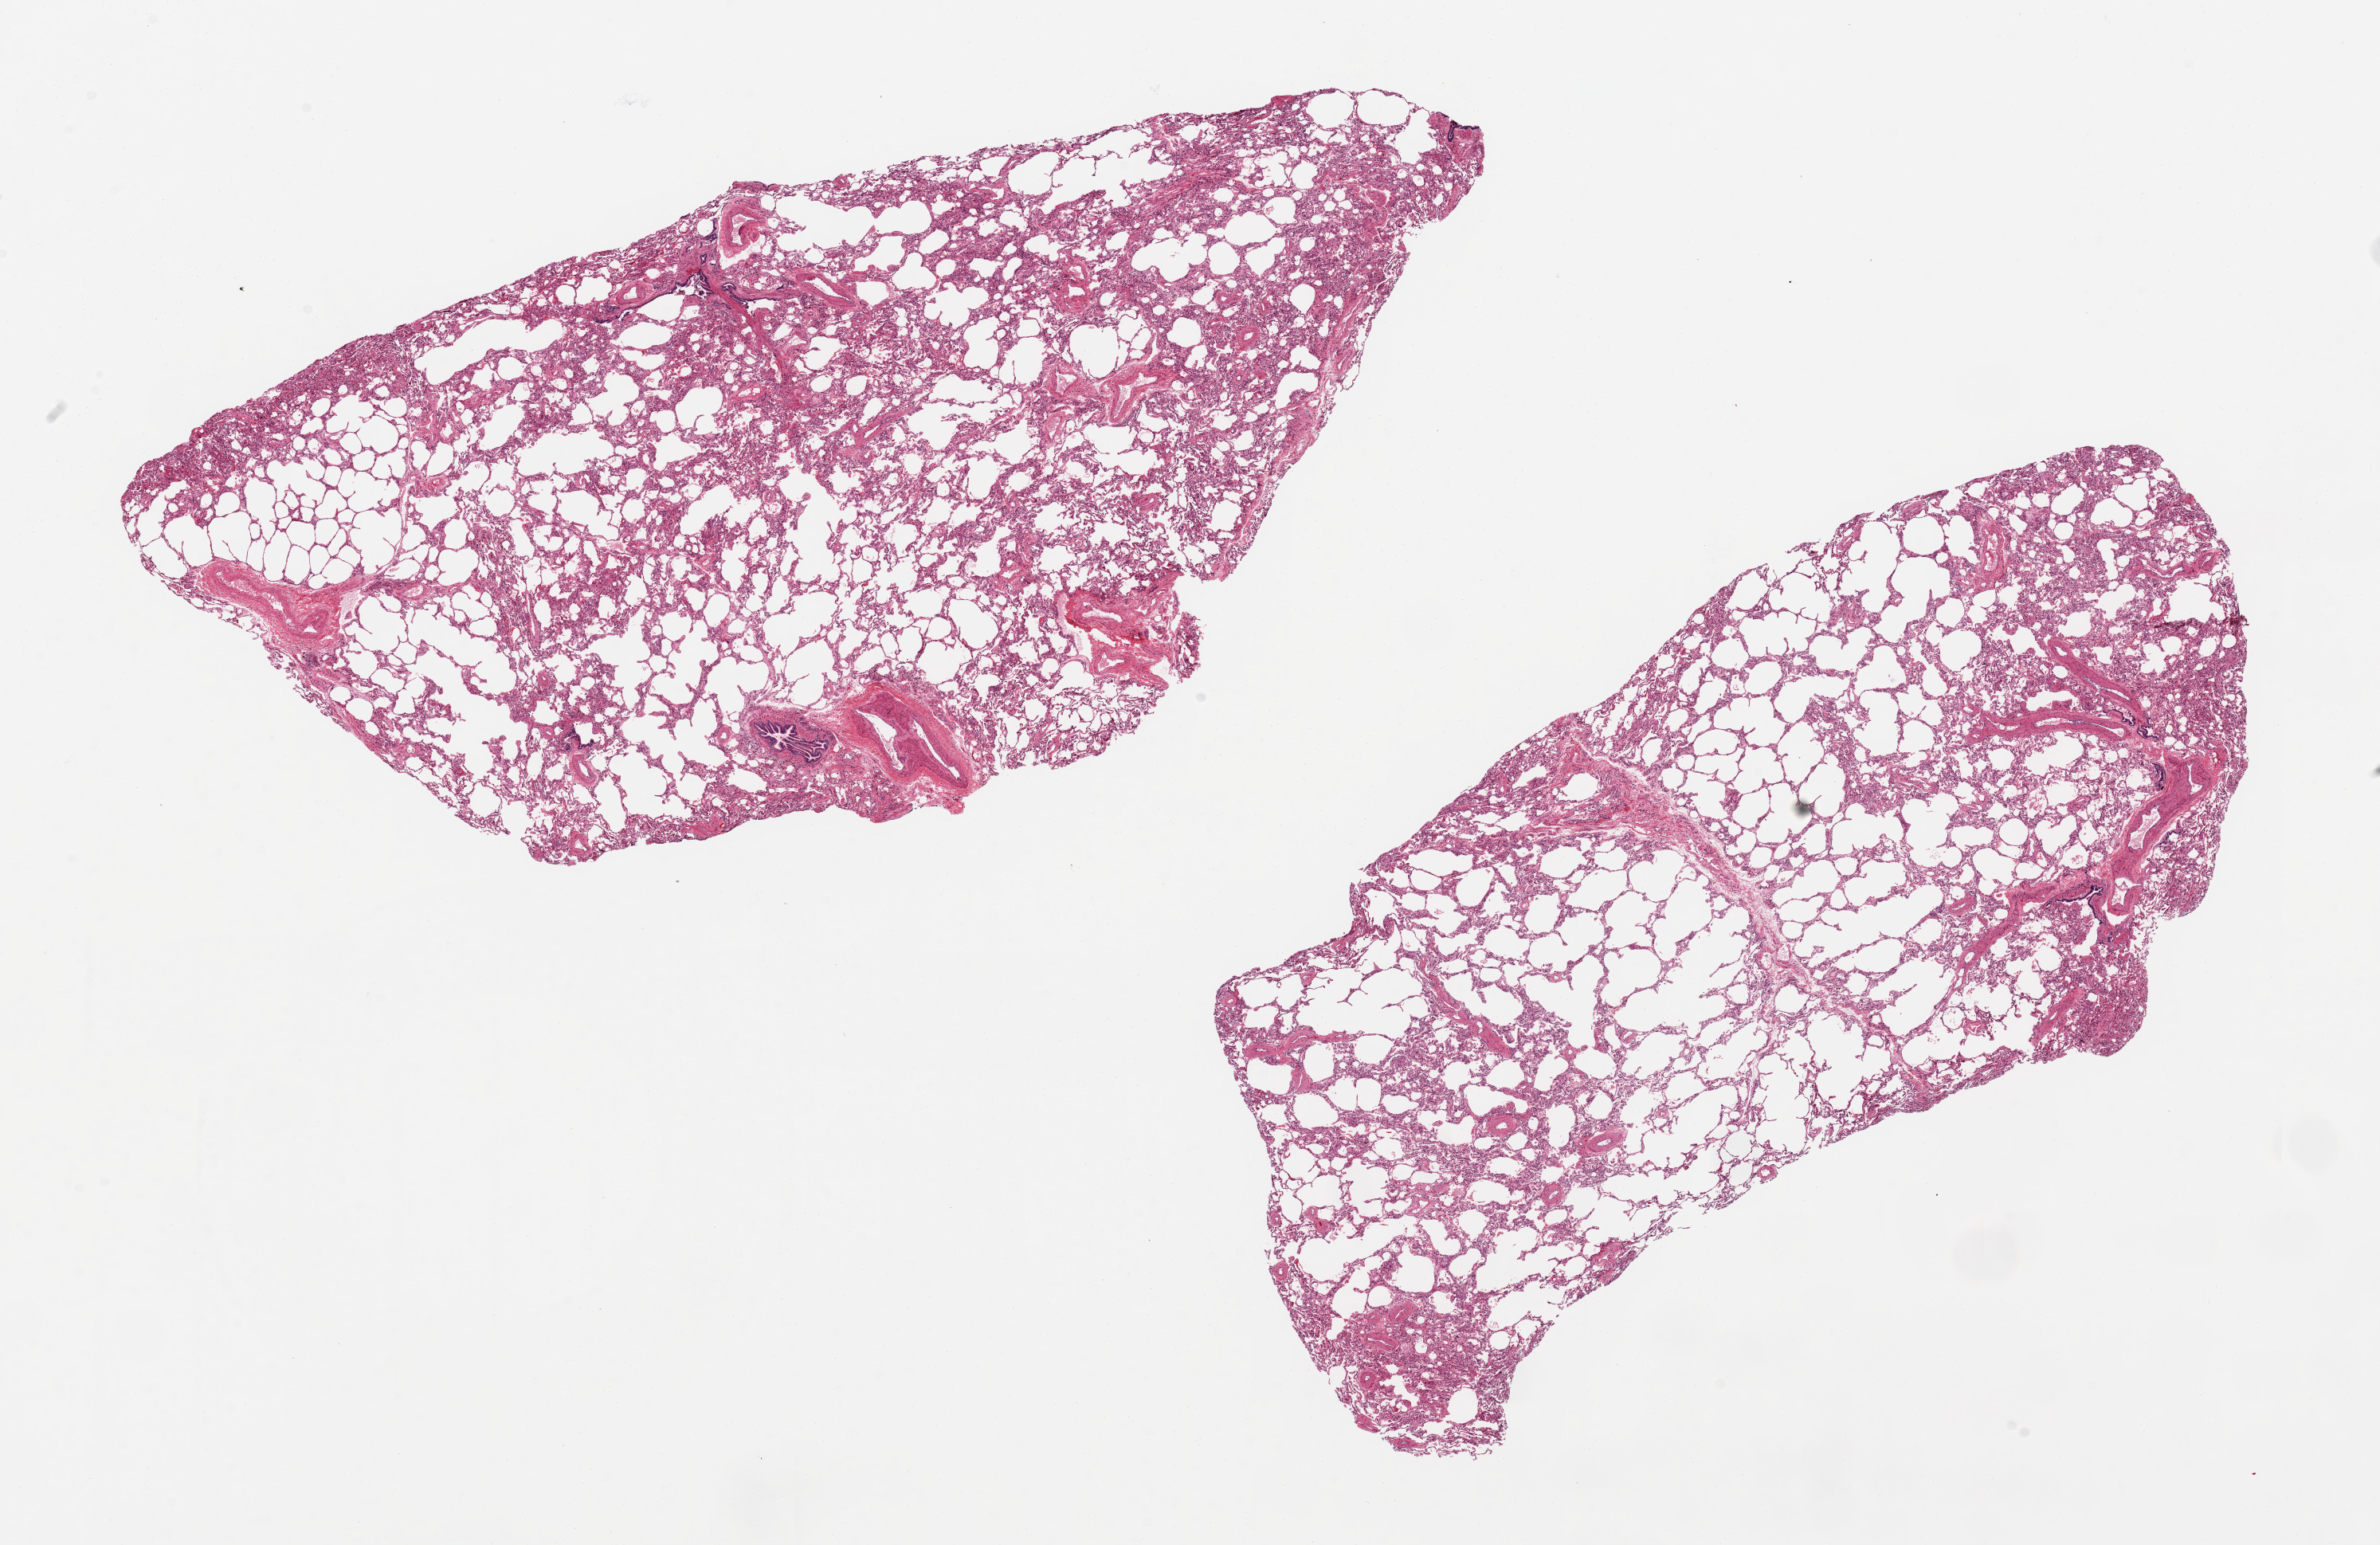
Whole-slide image, H&E stain — shown as a low-resolution overview of the whole scanned area (about 23.6 x 15.3 mm), PAXgene-fixed, paraffin-embedded tissue, section of lung (target tissue), tissue donor sample. Male donor.
Reviewer comment on this tissue sample: 2 aliquots, ~12x6mm, minimal congestion, well - preserved.